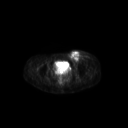
FDG PET of an extremity soft-tissue mass (from a PET/CT study), one axial slice. Position 72 of 267 along the scan axis. 3.27 mm slice thickness. 128 × 128 image matrix, field of view 600 × 600 mm. Female patient, age 24 years. From the clinical record (not read from this slice): histological type: leiomyosarcoma; grade: high; site of the primary tumour: groin.
Annotated regions visible in this slice (expert contour drawn on MRI and transferred to this co-registered scan by the dataset authors):
- gross tumour volume including surrounding oedema: box from (x=68, y=50) to (x=91, y=66) px
- gross tumour volume (mass): (x=68, y=50)–(x=82, y=63)